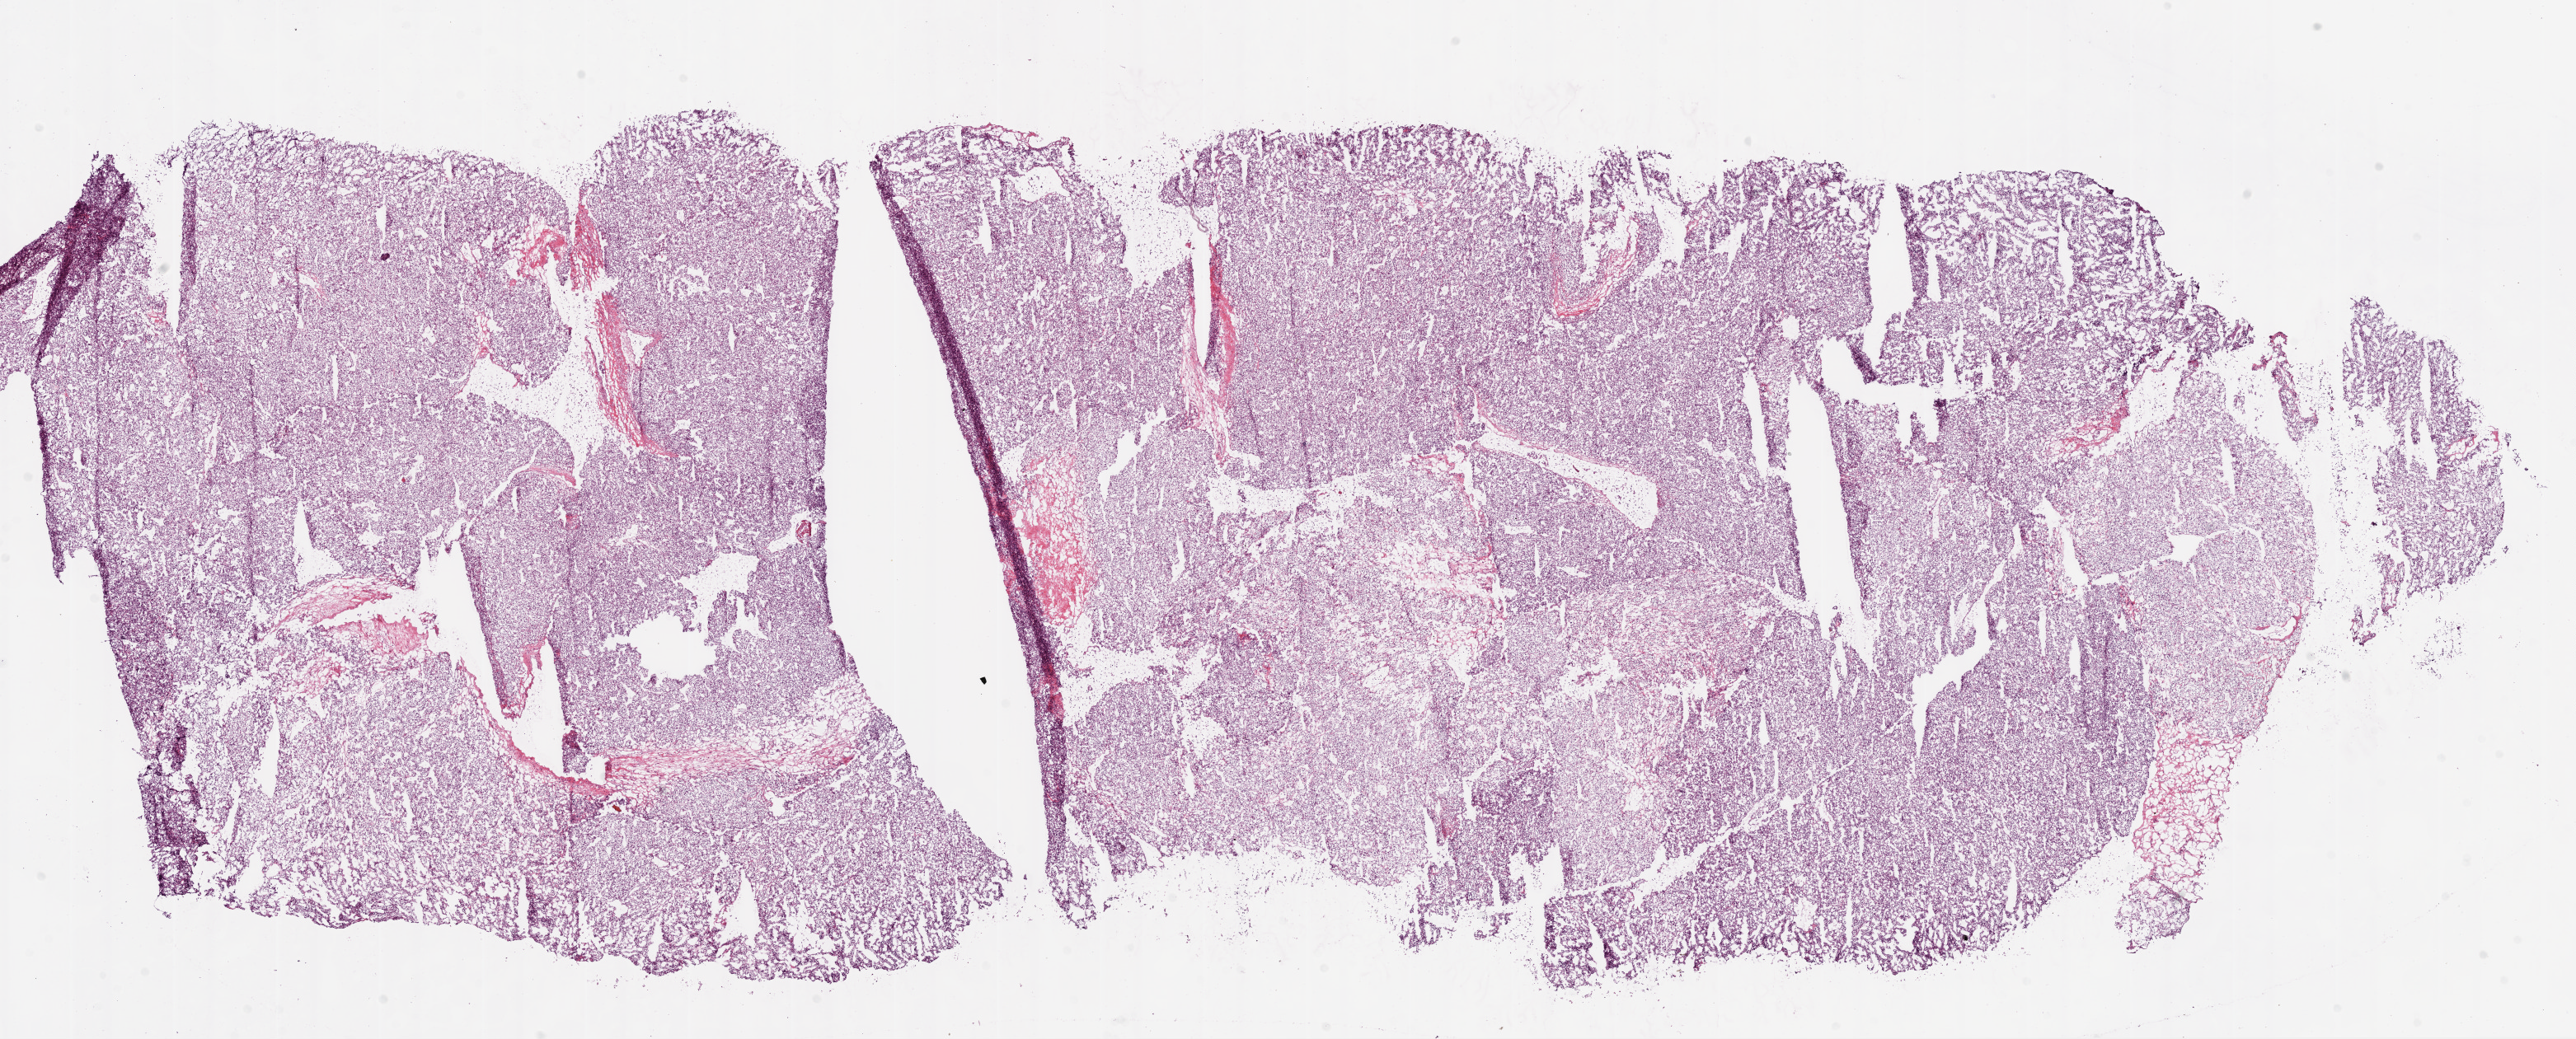
Digitized H&E tissue section (whole slide), low-resolution overview of the scanned area, about 25.1 x 10.1 mm, frozen section from the bottom of the tissue portion, primary tumour sample from the kidney. Female, age 71 years at initial diagnosis. Histologic grade: G2 (moderately differentiated). Pathologist review of this section (percent, as recorded): tumour cells 95%, tumour nuclei 90%, normal cells 0%, stromal cells 5%, necrosis 0%.
Pathologic diagnosis: Clear cell adenocarcinoma, NOS. Laterality: left. AJCC pathologic stage: III.